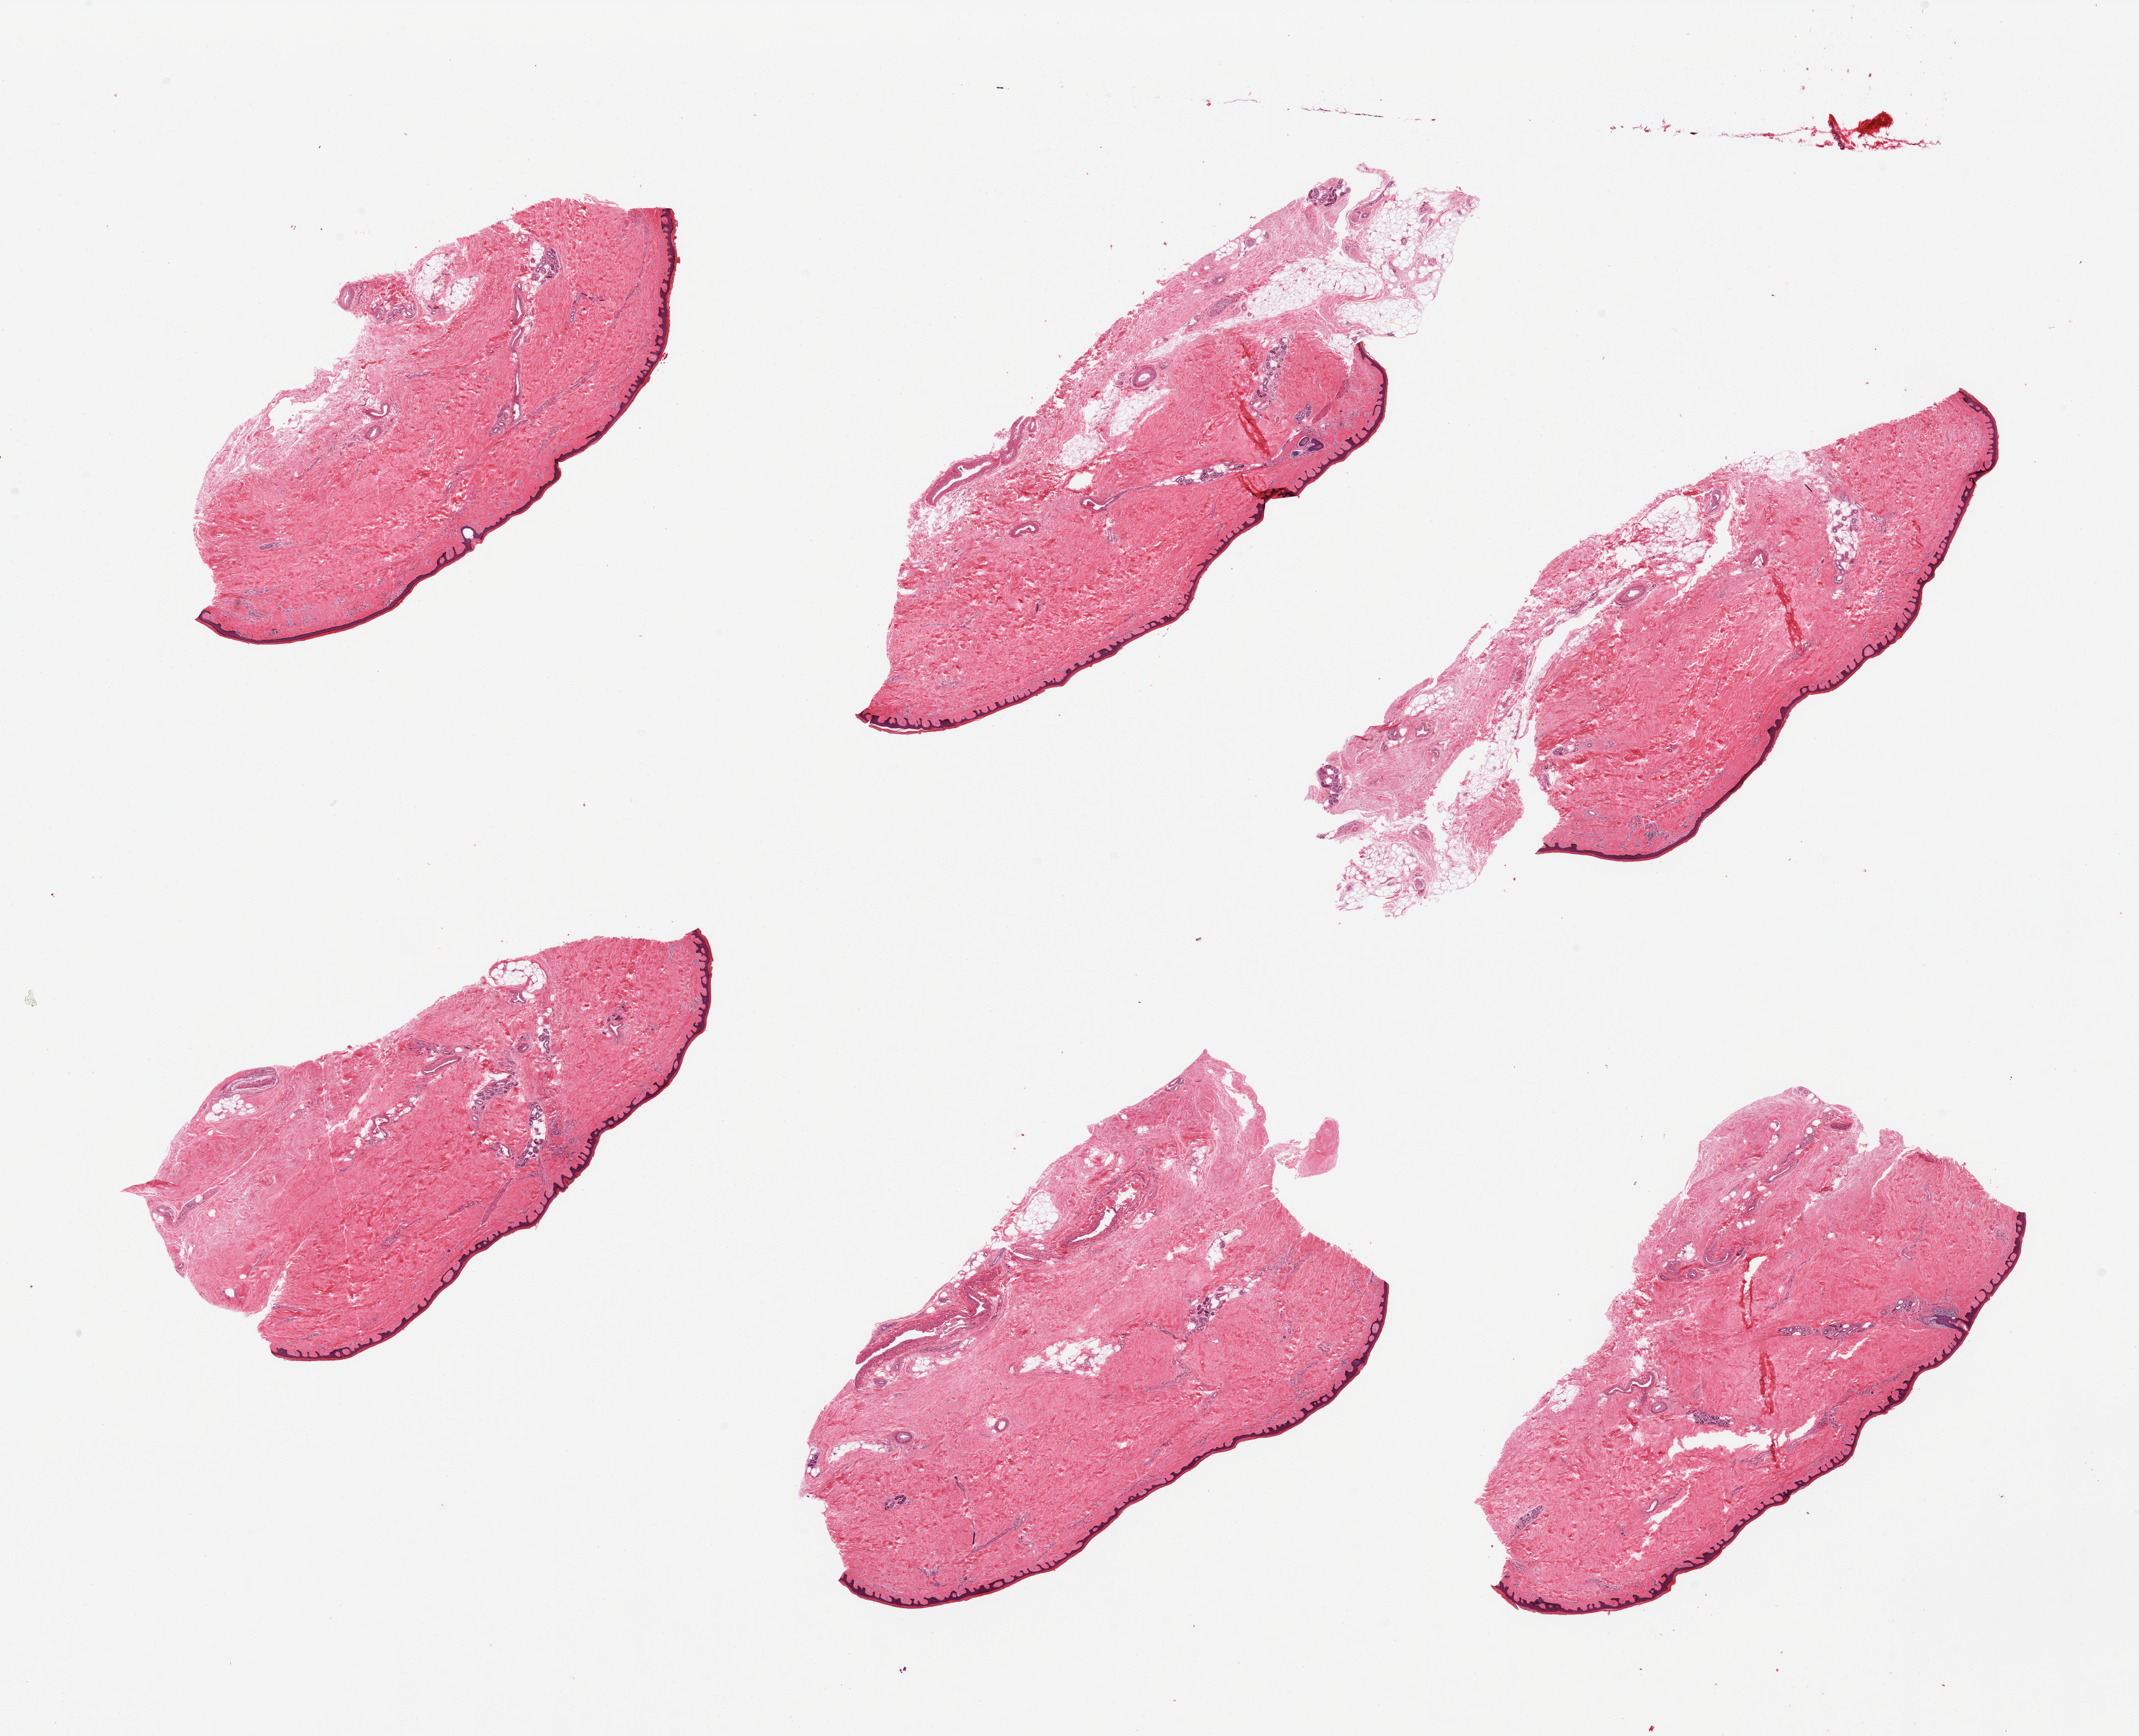
Digitized hematoxylin and eosin (H&E)-stained section, whole scanned area (about 26.6 x 21.6 mm, slide scanned at 20x) shown as a low-resolution overview; PAXgene-fixed paraffin-embedded (PFPE) section; sampled site (target tissue): skin of lower leg; donor tissue sample. Donor sex: male.
• review note (as recorded): 6 pieces, predominantly well trimmed, but 2 with attached and internal fat up to ~10%, squamous epithelium measures 25-50 microns